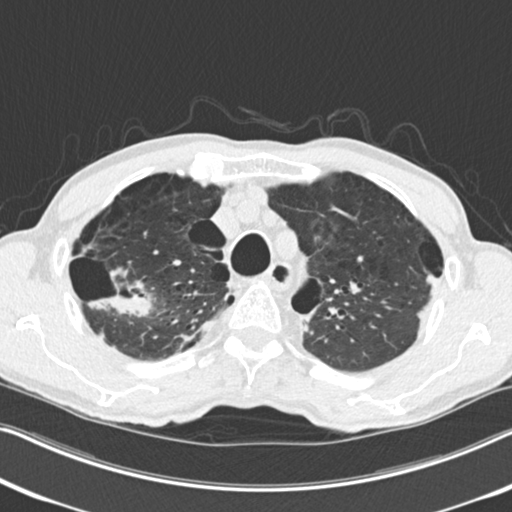
Low-dose screening chest CT, one axial slice. Position 198 of 251 along the scan axis. Reconstruction kernel B30f. 120 kVp. Lung window (W 1500 / L -600 HU). 2 mm slice thickness. 512 × 512 image matrix.
Structures marked on this image (expert manual segmentation):
- lesion 1 (tumor, upper lobe of right lung): box from (x=89, y=288) to (x=153, y=317) px